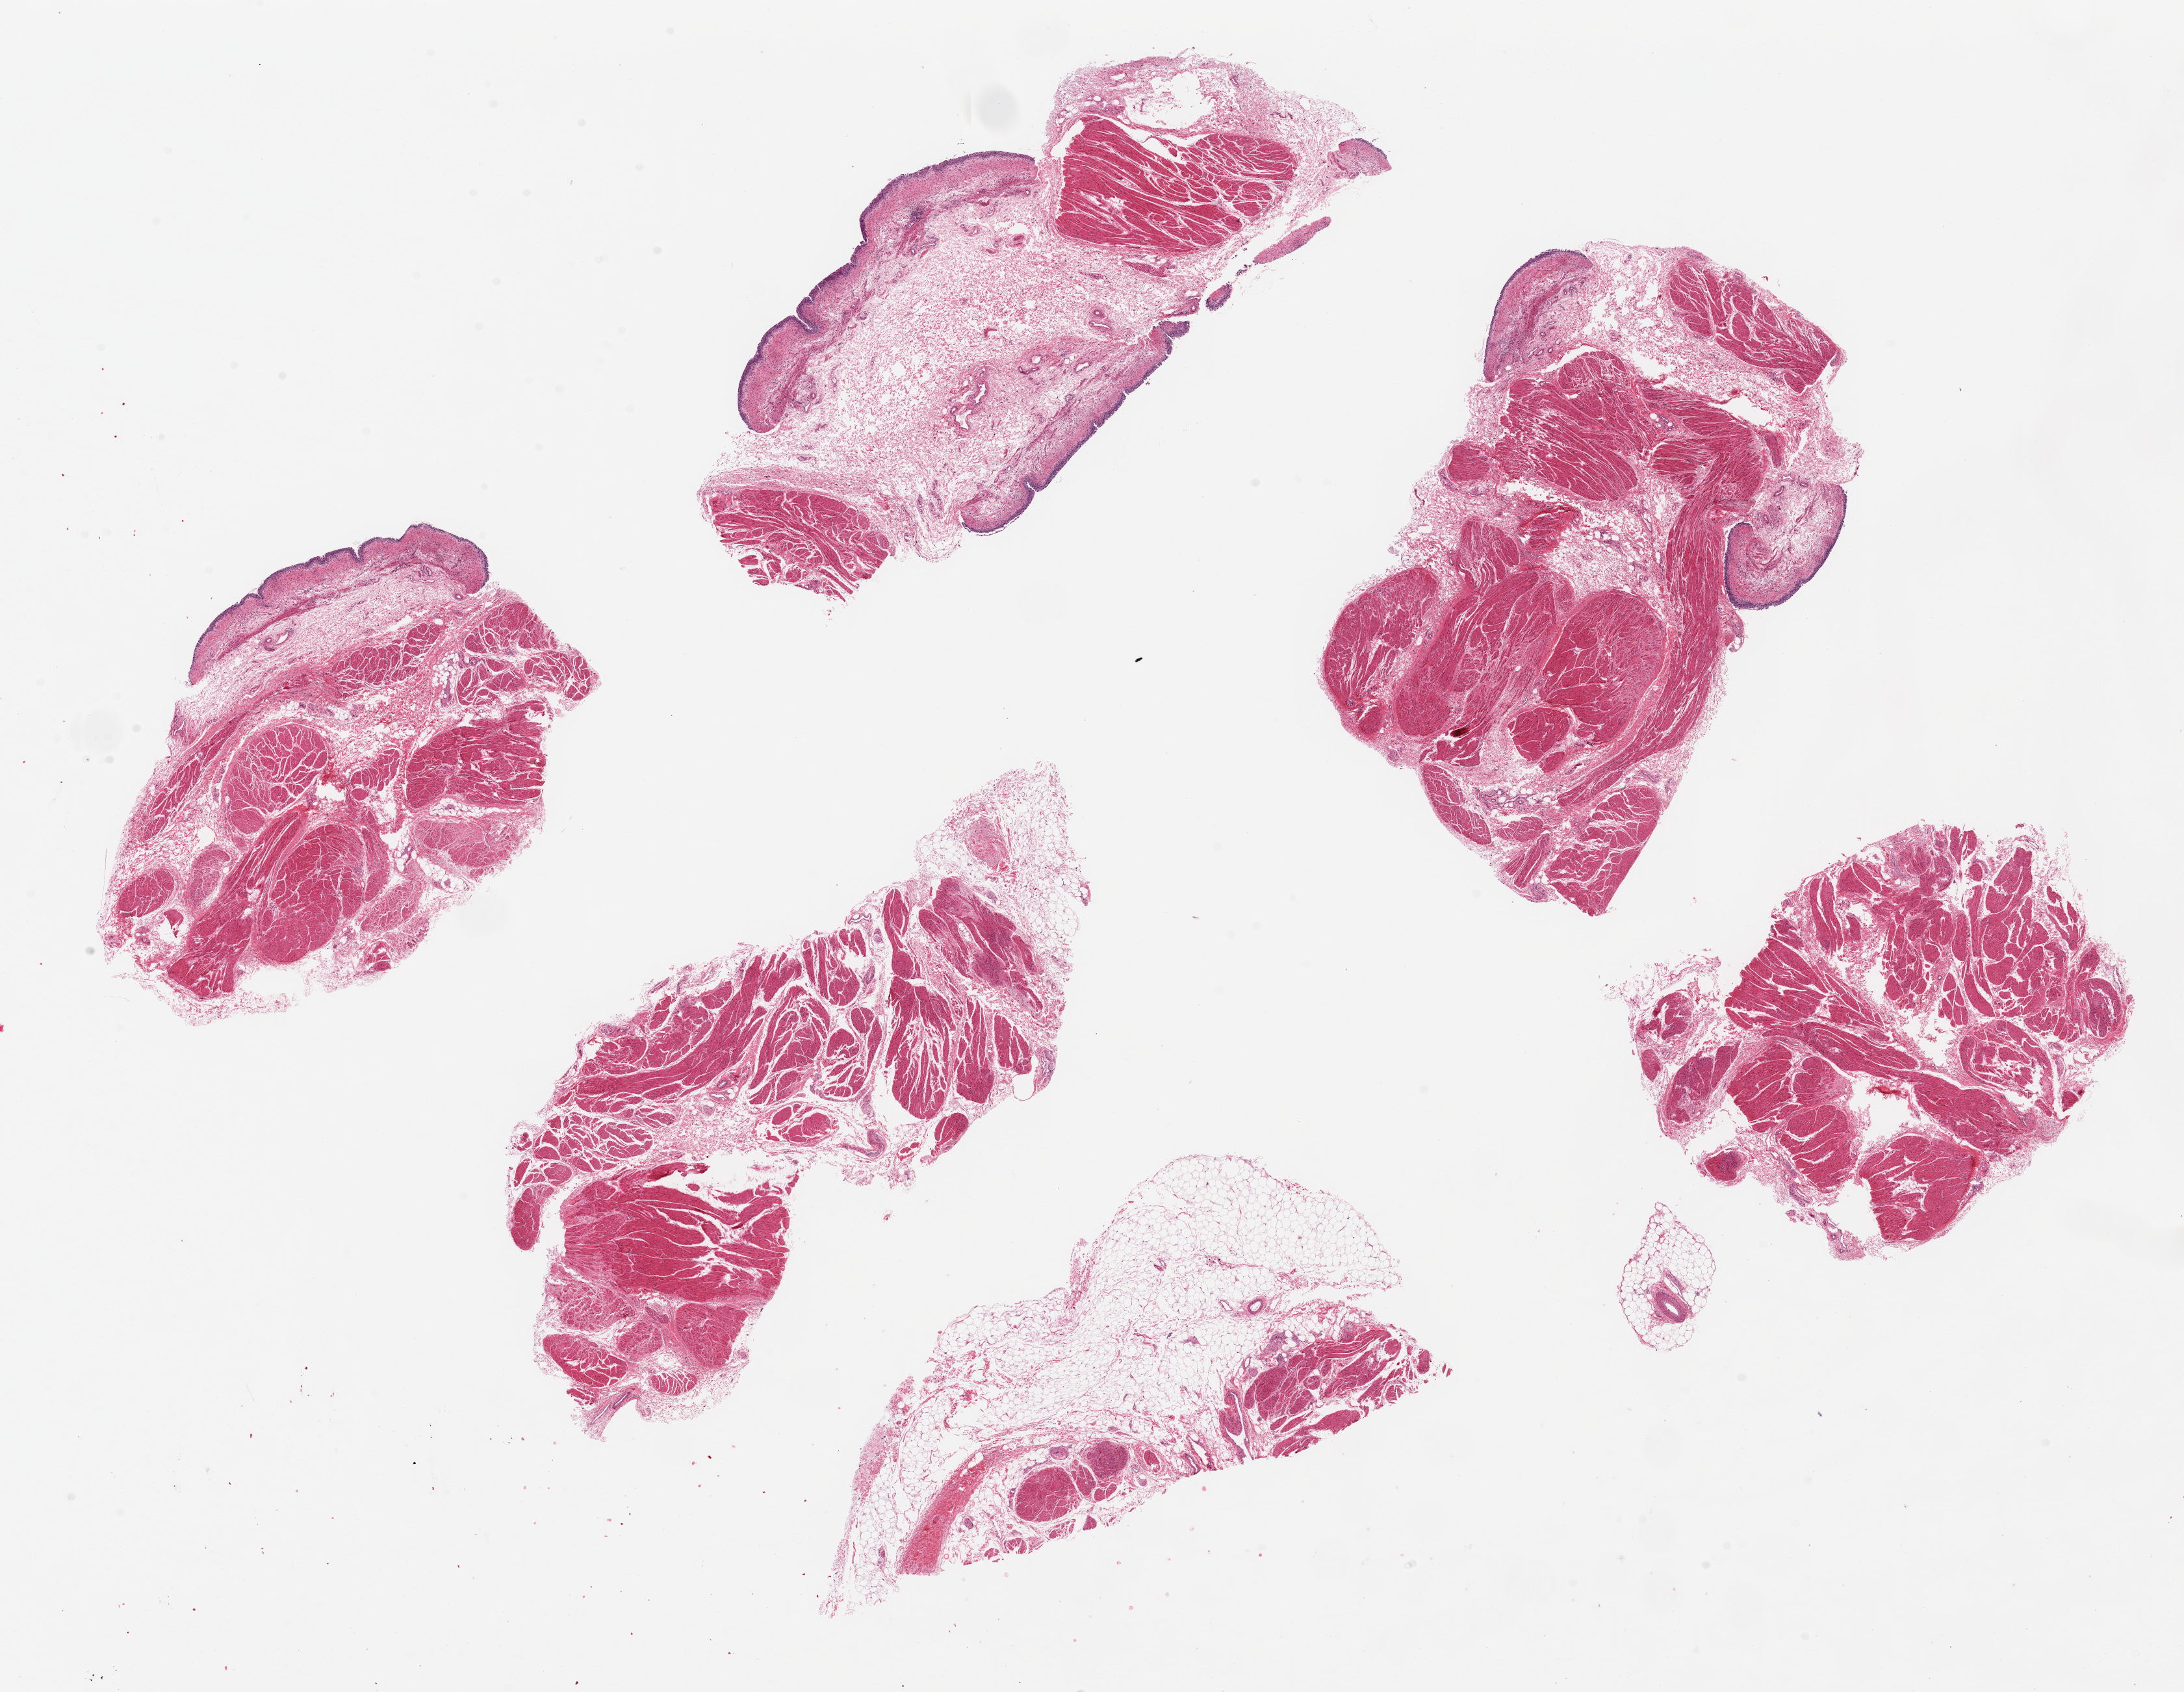
Digitized hematoxylin and eosin (H&E)-stained section, brightfield — low-resolution overview of the scanned area, about 26.6 x 20.6 mm (slide scanned at 20x). PAXgene-fixed paraffin-embedded (PFPE) section. Target tissue: urinary bladder. Donor tissue sample. Donor: female.
• review note (as recorded): 6 pieces, urothelium sparse and ~ 1% of thickness where visible (focal in 3of 6 aliquots, ~7x3.5mm)